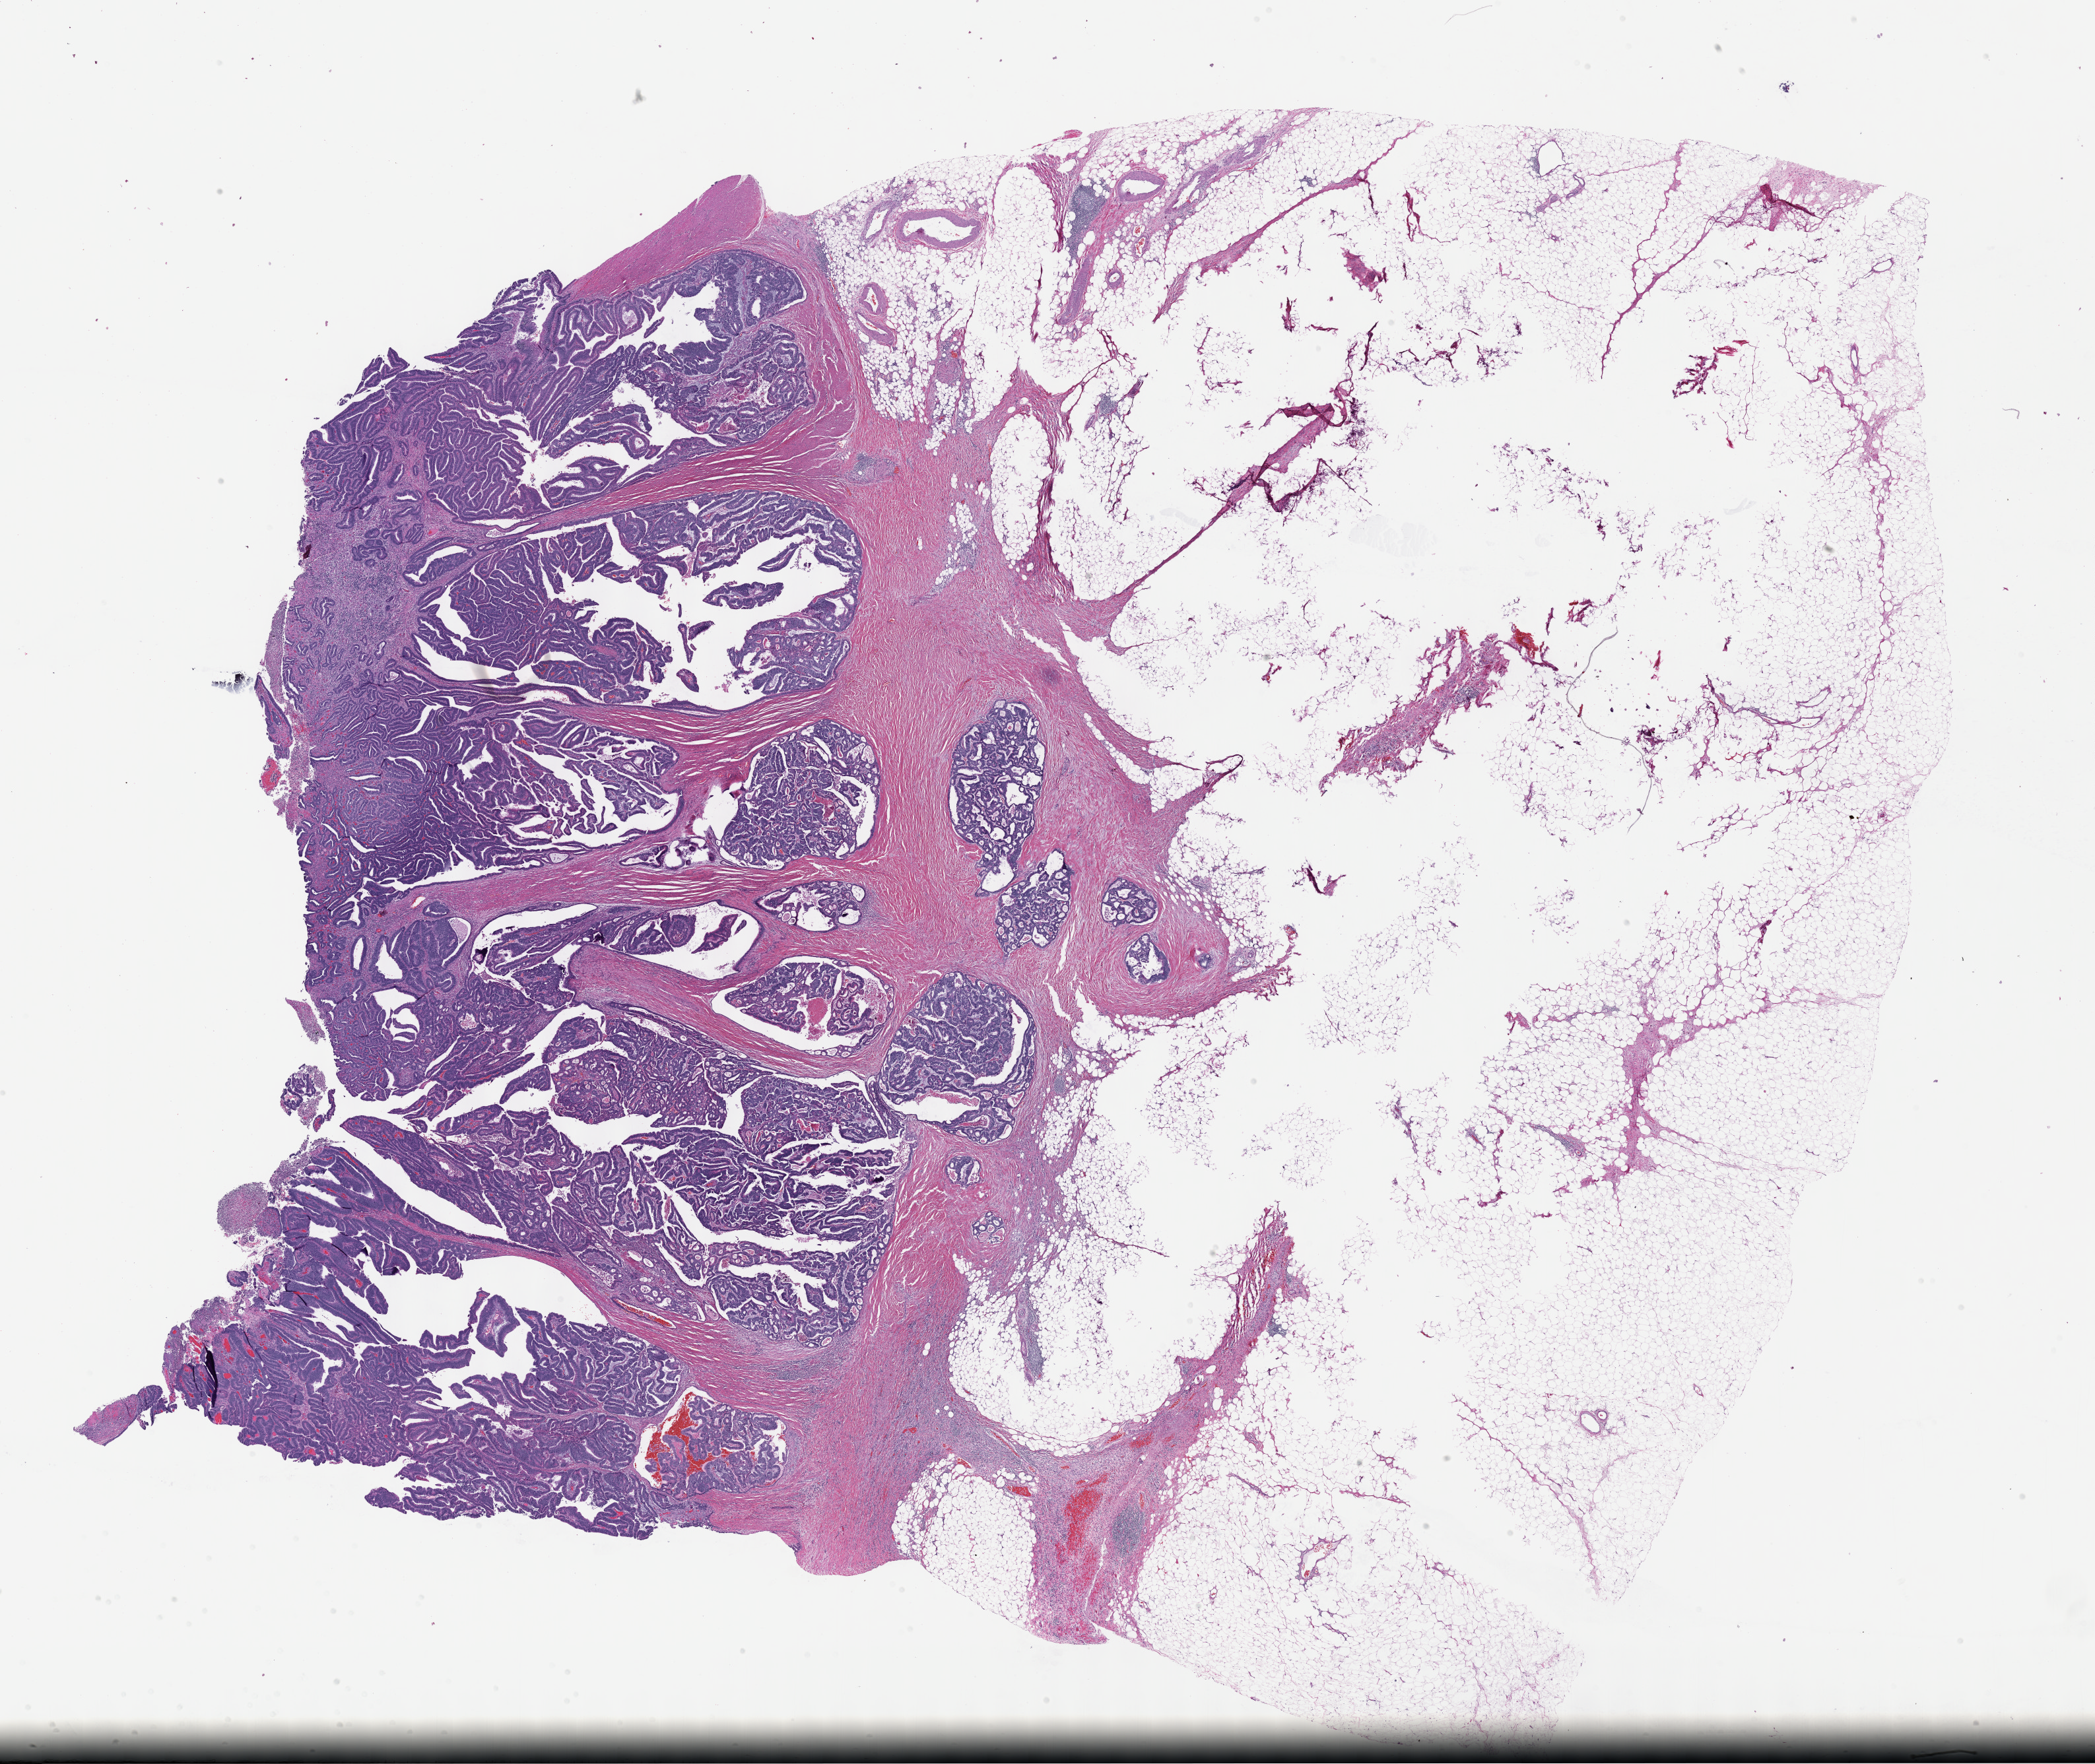
H&E-stained whole-slide image, low-resolution overview of the scanned area, about 25.7 x 21.6 mm (acquisition: 40x scan), formalin-fixed paraffin-embedded (FFPE) diagnostic section, sample: primary tumour, colon. Patient: female, age at initial diagnosis 53 years.
Diagnosis: Adenocarcinoma, NOS (sigmoid colon). AJCC pathologic stage: IIA (7th edition). TNM: T3 N0 MX. Lymph nodes positive (case pathology): 0 of 18 examined.